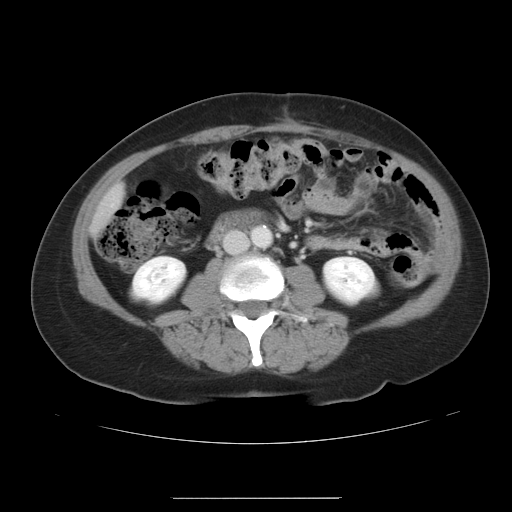
Contrast-enhanced abdominal CT, one axial slice; position 7 of 41 along the scan axis; soft-tissue window (W 400 / L 40 HU); 5 mm slice thickness; 512 × 512 image matrix, field of view 381 × 381 mm. Female patient, age 63 years. Case-level facts recorded for this patient, not image findings: diagnosis: colorectal cancer liver metastases, imaged before liver resection; multiple liver metastases: yes; largest metastasis: 1.5 cm; disease in both lobes: yes.
Outlined on this slice (expert manual segmentation):
- liver: bounding box (x1, y1, x2, y2) in pixels: (94, 188, 124, 231)
- planned liver remnant (the part of the liver to remain after resection): (94, 188, 124, 231)